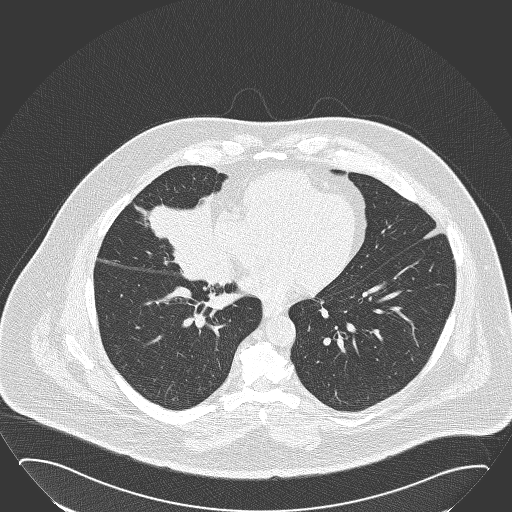
Axial slice from a low-dose chest CT screening exam. Baseline screening round. Lung window (W 1500 / L -600 HU). Slice 98 of 168 in the series. 512 × 512 image matrix. Male participant, aged 61 years at enrolment.
Lesion marked by an expert reader, bounding box [x1, y1, x2, y2] px = [139, 185, 229, 273]. The screening reader recorded 2 non-calcified nodules or masses ≥4 mm on this exam (right middle lobe, left lower lobe); which of them this box marks is not recorded. Official screen result: positive, change unspecified: nodule(s) >= 4 mm or enlarging nodule(s), mass(es), or other non-specific abnormalities suspicious for lung cancer. Lung cancer was diagnosed 47 days after this screen: basaloid squamous cell carcinoma, right middle lobe, right hilum, poorly differentiated (G3), stage IIB (AJCC 6th edition), 95 mm at pathology.